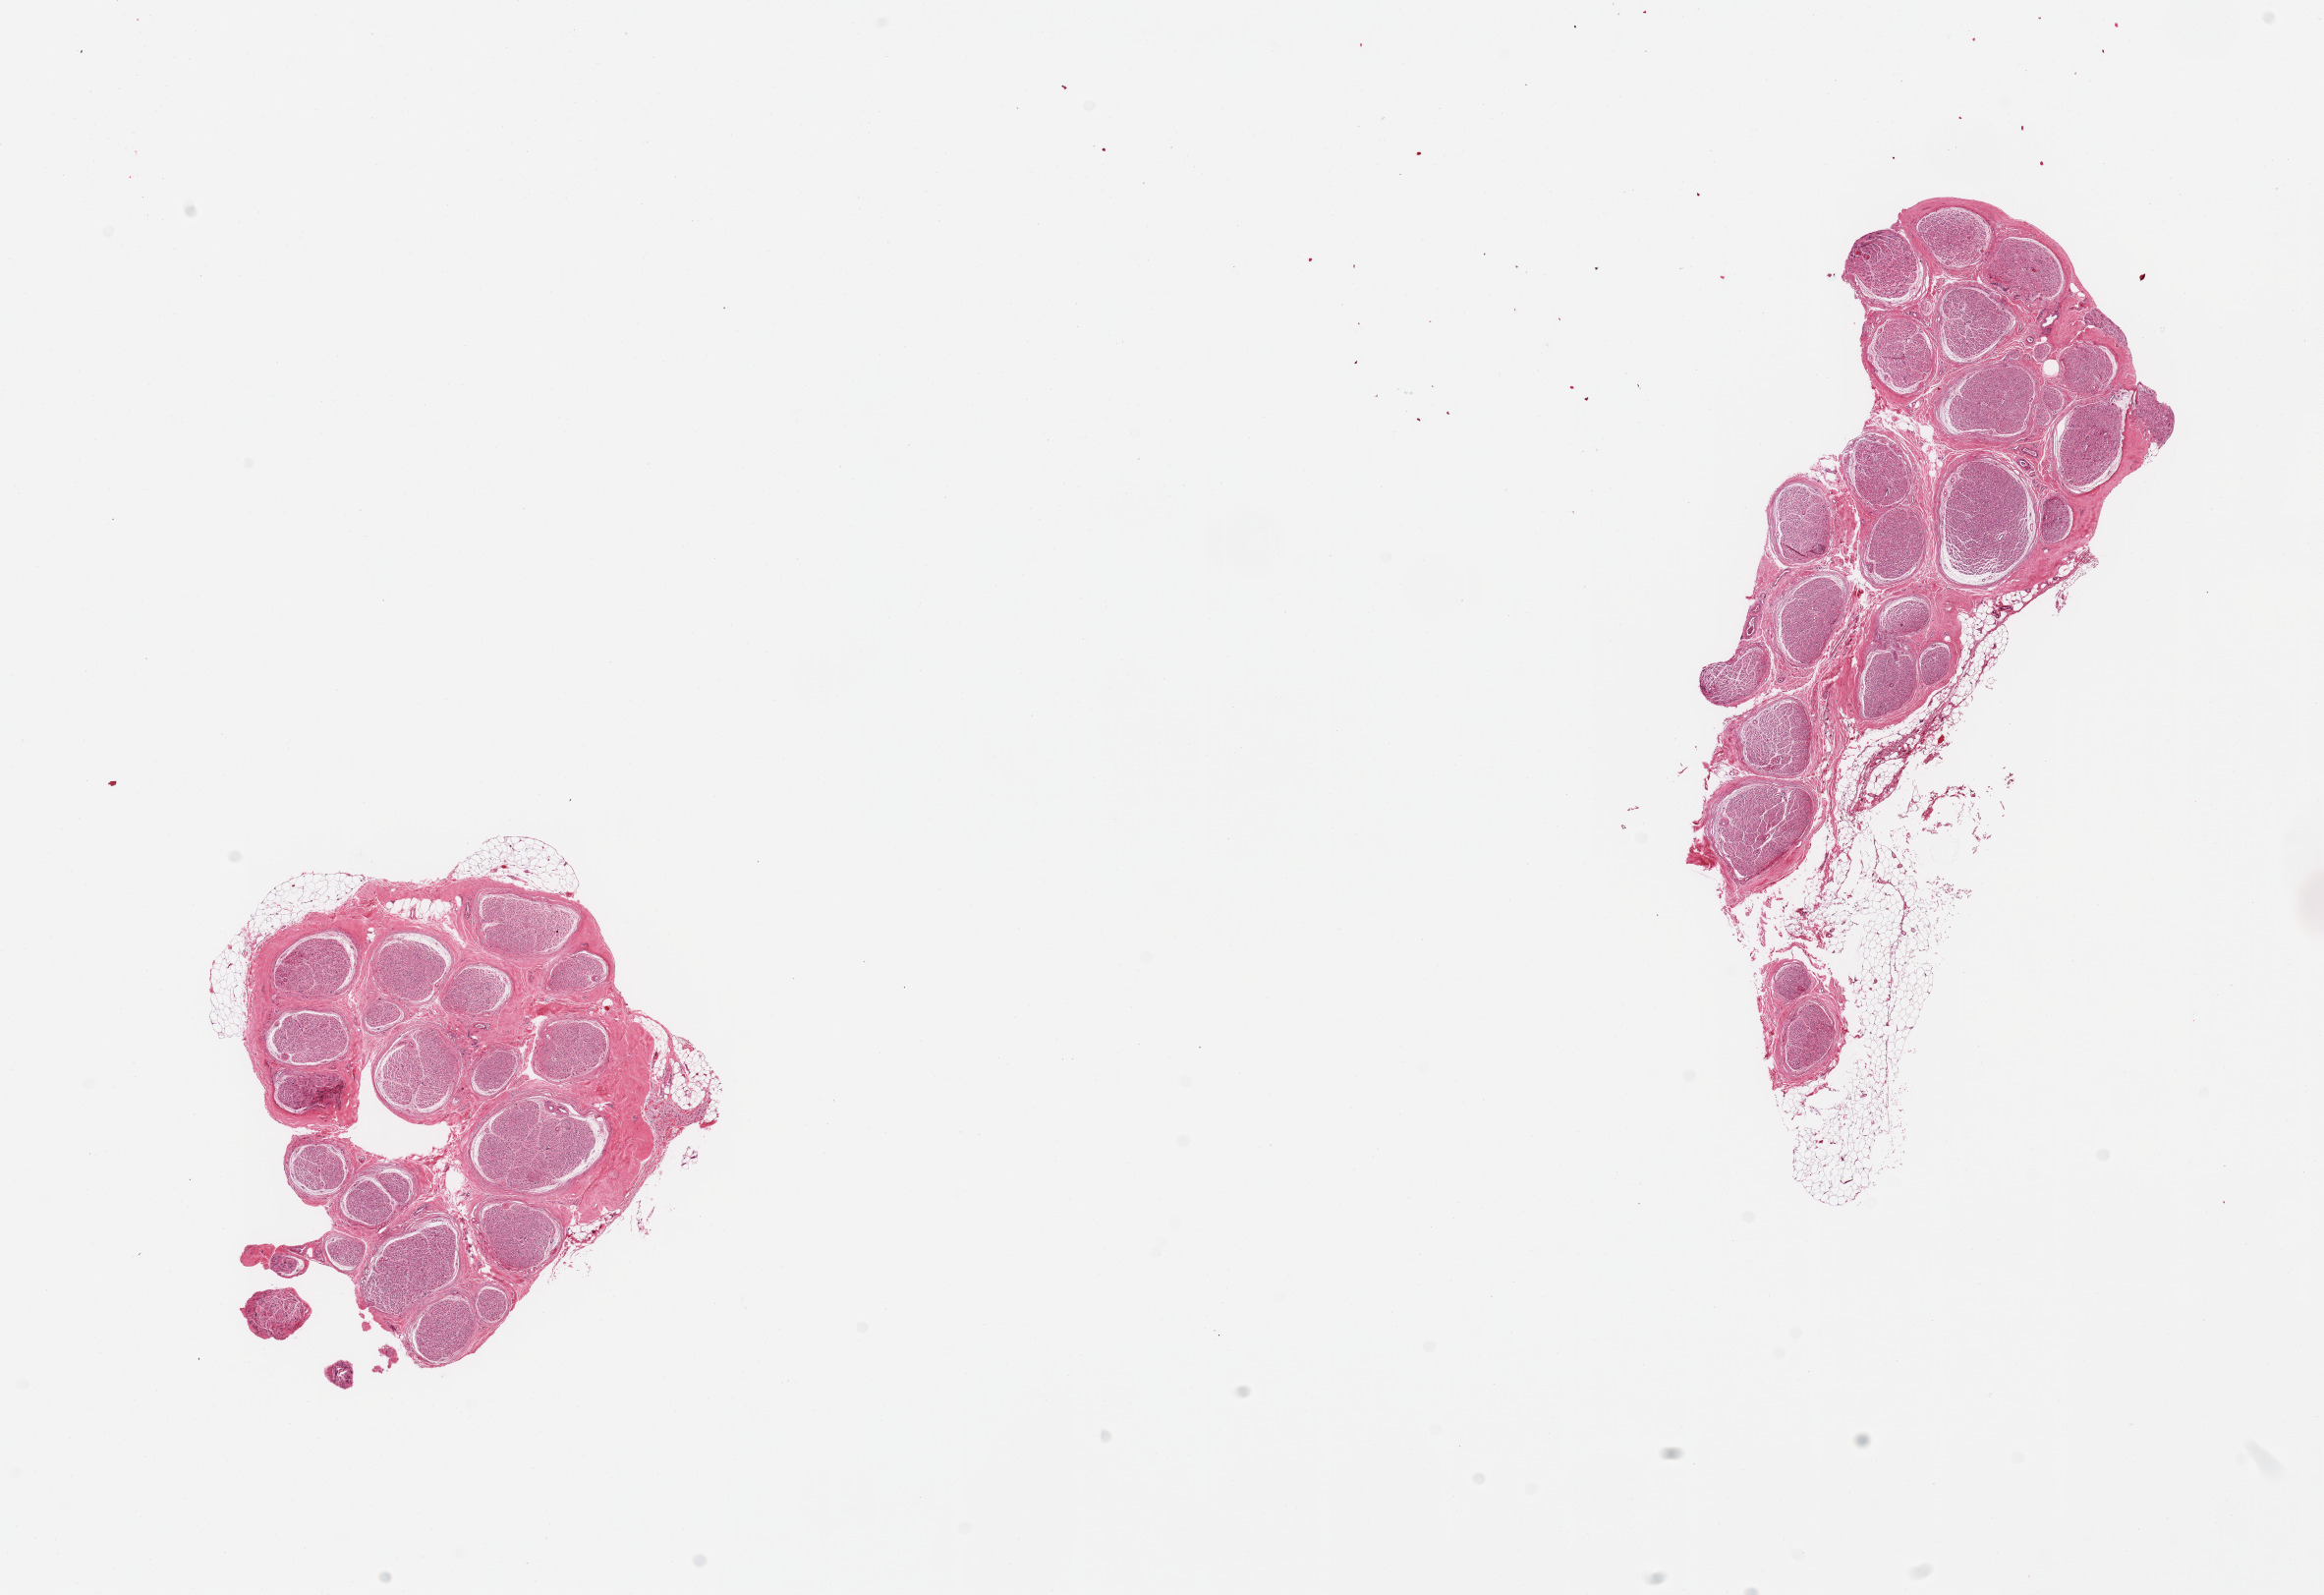
H&E whole-slide image — low-resolution overview of the scanned area, about 18.7 x 12.8 mm, PAXgene-fixed, paraffin-embedded tissue, target tissue: tibial nerve, tissue donor sample. Male donor.
• pathologist's review note for this sample: 2 pieces; 1 piece has ~10% attached fat